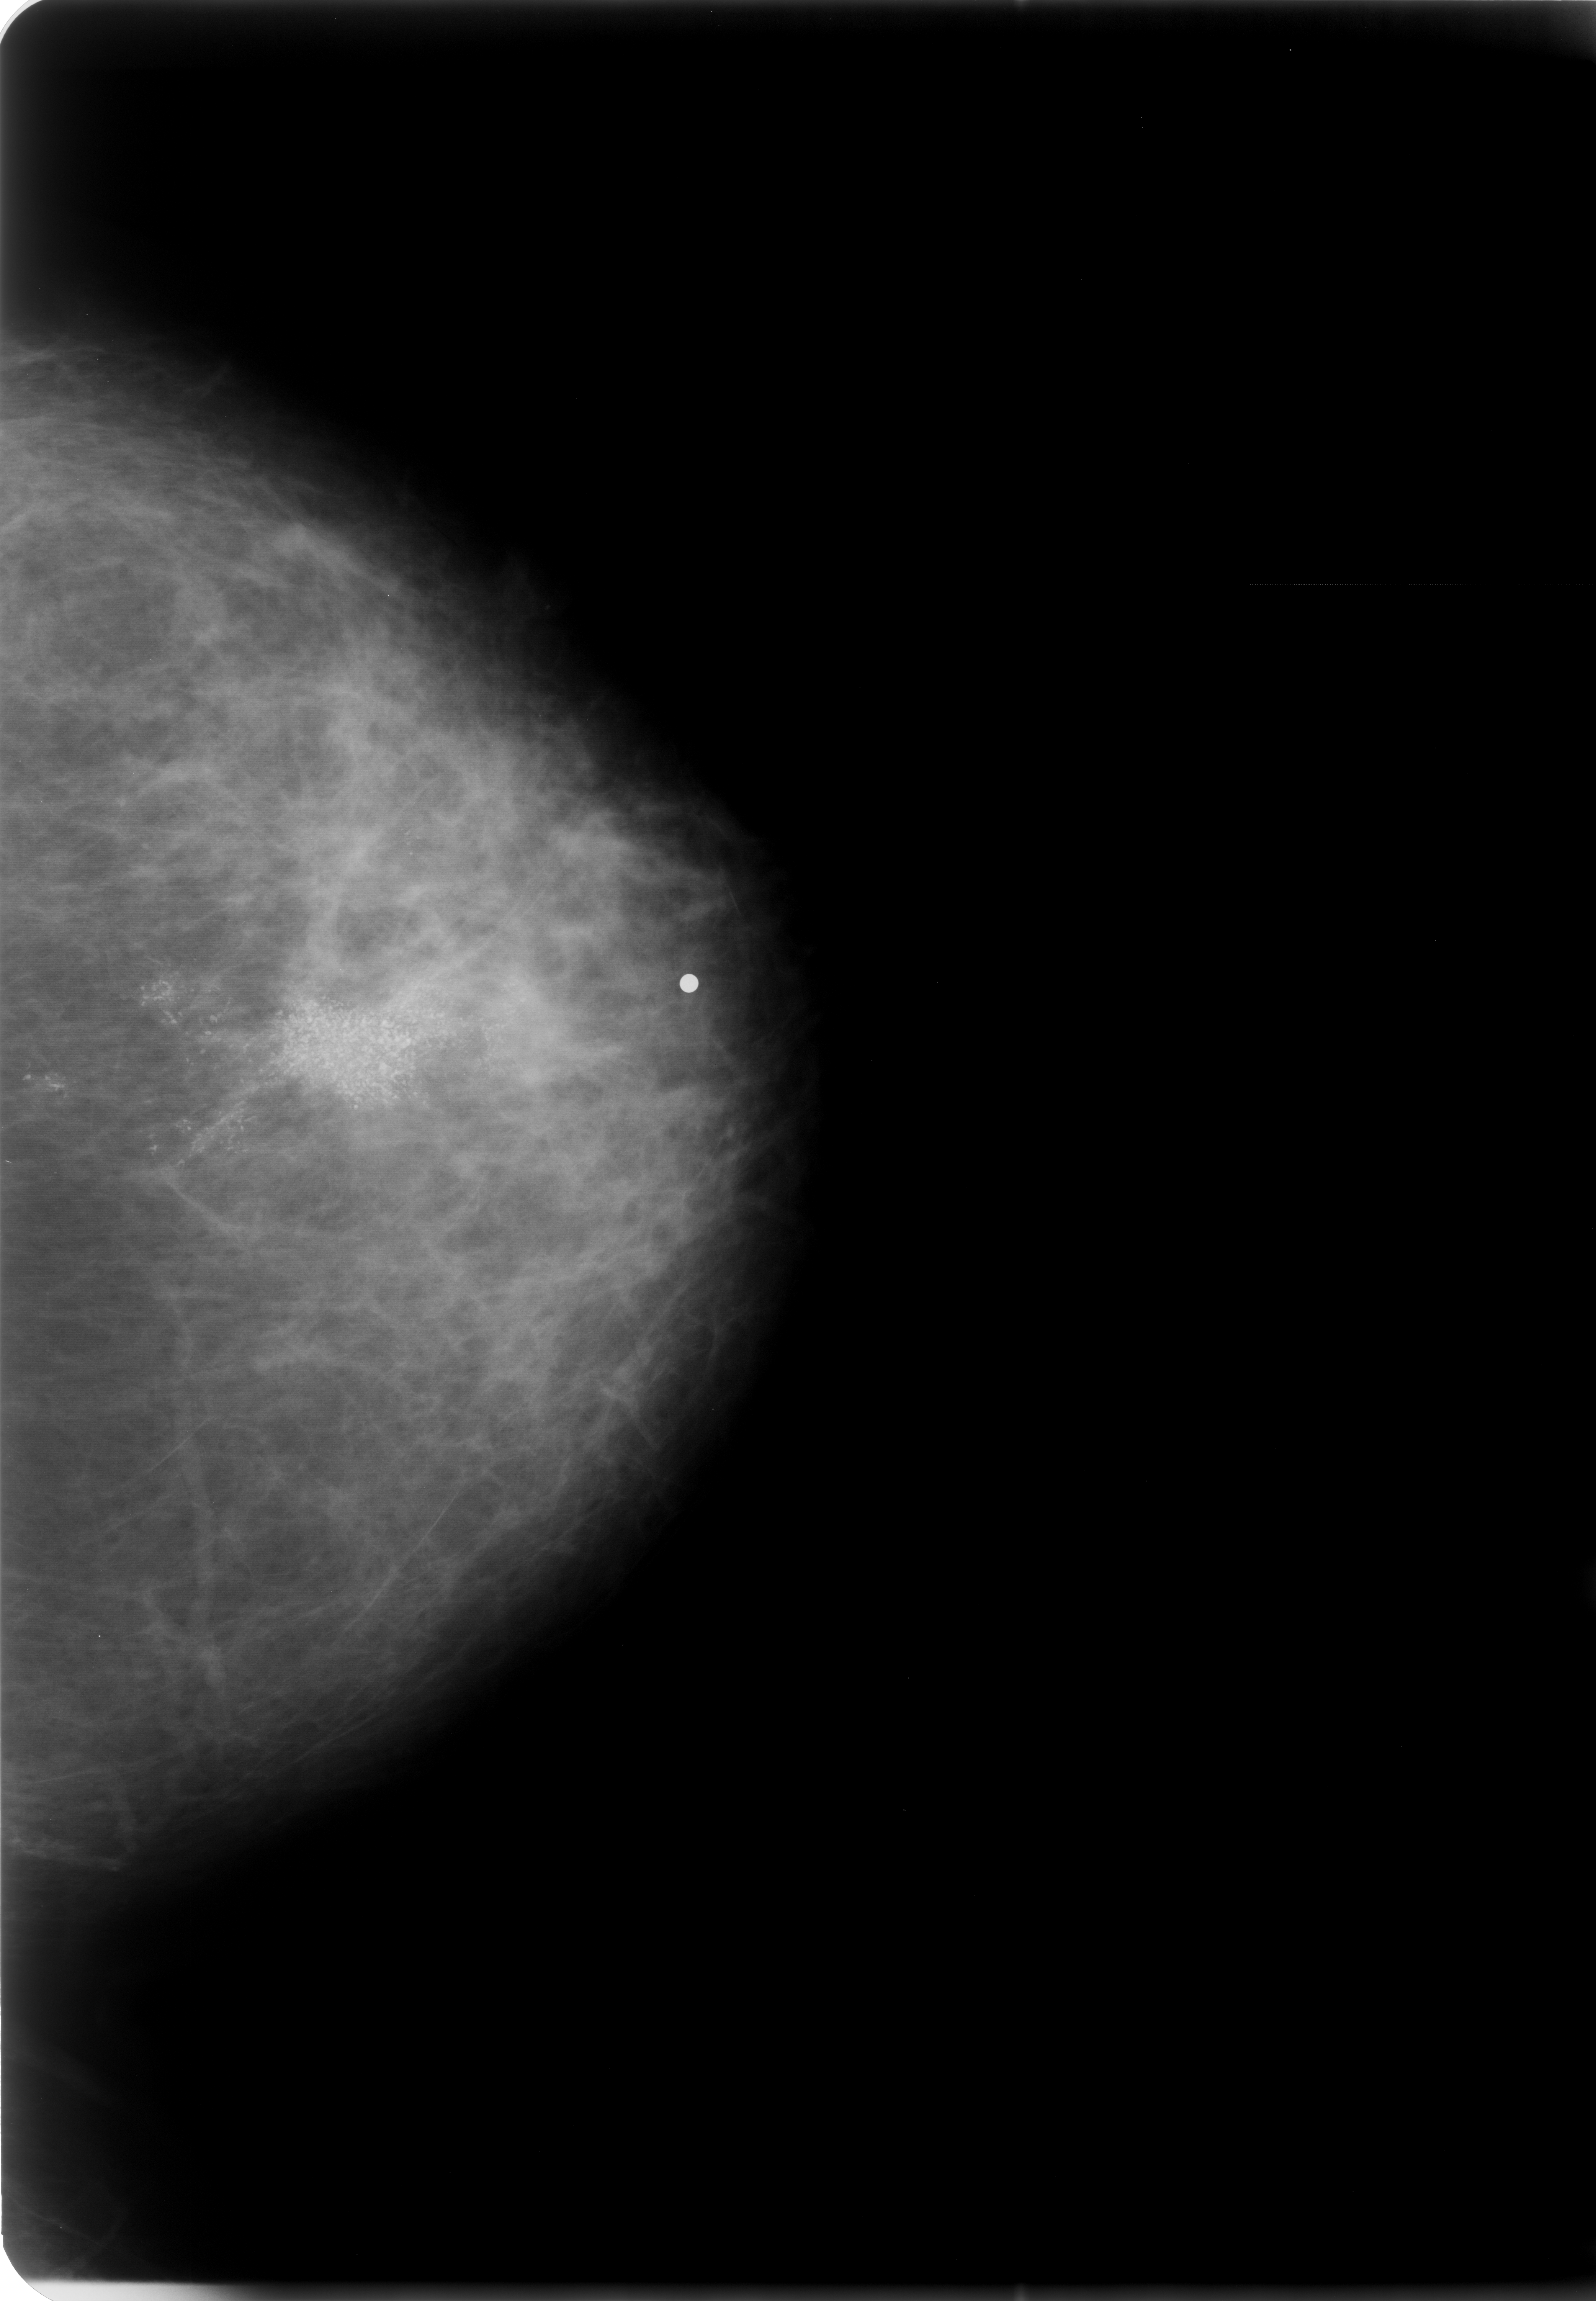
Mammogram (digitized film). Left breast. CC view. Breast composition: scattered fibroglandular densities (BI-RADS density category 2 of 4). 1596 × 2301 image matrix.
Marked abnormalities (boxes around the expert regions of interest):
- calcifications, morphology pleomorphic, distribution segmental; BI-RADS assessment category 5; pathology result (as recorded, not read from the image): malignant: bounding box <6,811,598,1334> (left, top, right, bottom; pixels)